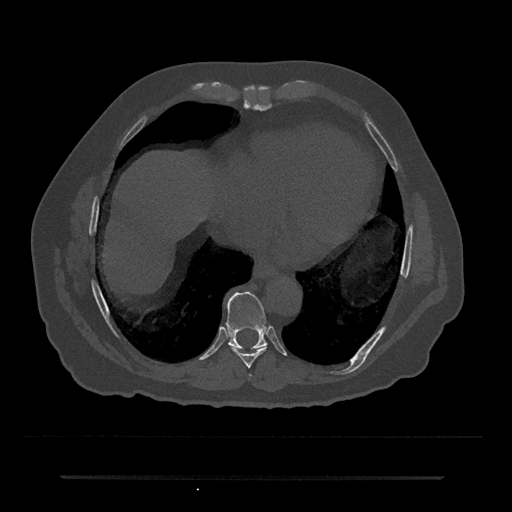
CT including the spine, one axial slice. Slice 306 of 797 in the series (ordered by position). Reconstruction kernel Br40s/3. 120 kVp. Bone window (W 1800 / L 400 HU). 0.5 mm slice thickness. 512 × 512 image matrix, field of view 437 × 437 mm. Male patient, age 69 years. Case-level facts recorded for this patient, not image findings: primary cancer: prostate.
Annotated regions visible in this slice (semi-automatically segmented with operator editing):
- T8 vertebra: bounding box (x1, y1, x2, y2) in pixels: (230, 346, 267, 367)
- T9 vertebra: (226, 291, 267, 350)